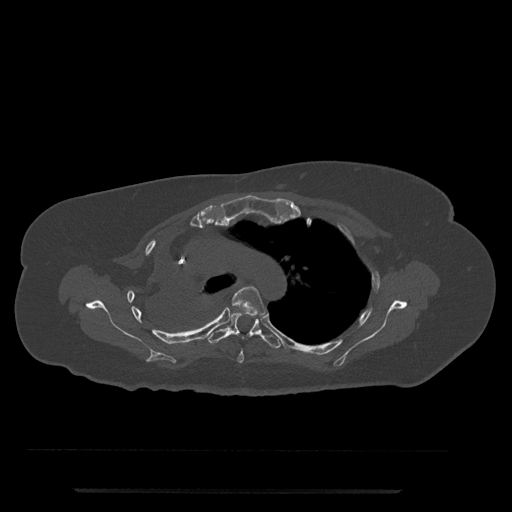
CT including the spine, one axial slice. Slice 563 of 797 in the series (ordered by position). Reconstruction kernel Br40s/3. 120 kVp. Bone window (W 1800 / L 400 HU). 0.5 mm slice thickness. 512 × 512 image matrix. Female patient, age 51 years. From the clinical record (not read from this slice): primary cancer: neuro.
Outlined on this slice (semi-automatic segmentation, software-assisted and operator-edited):
- T4 vertebra: box from (x=228, y=286) to (x=266, y=363) px
- T5 vertebra: (x=206, y=307)–(x=282, y=349)